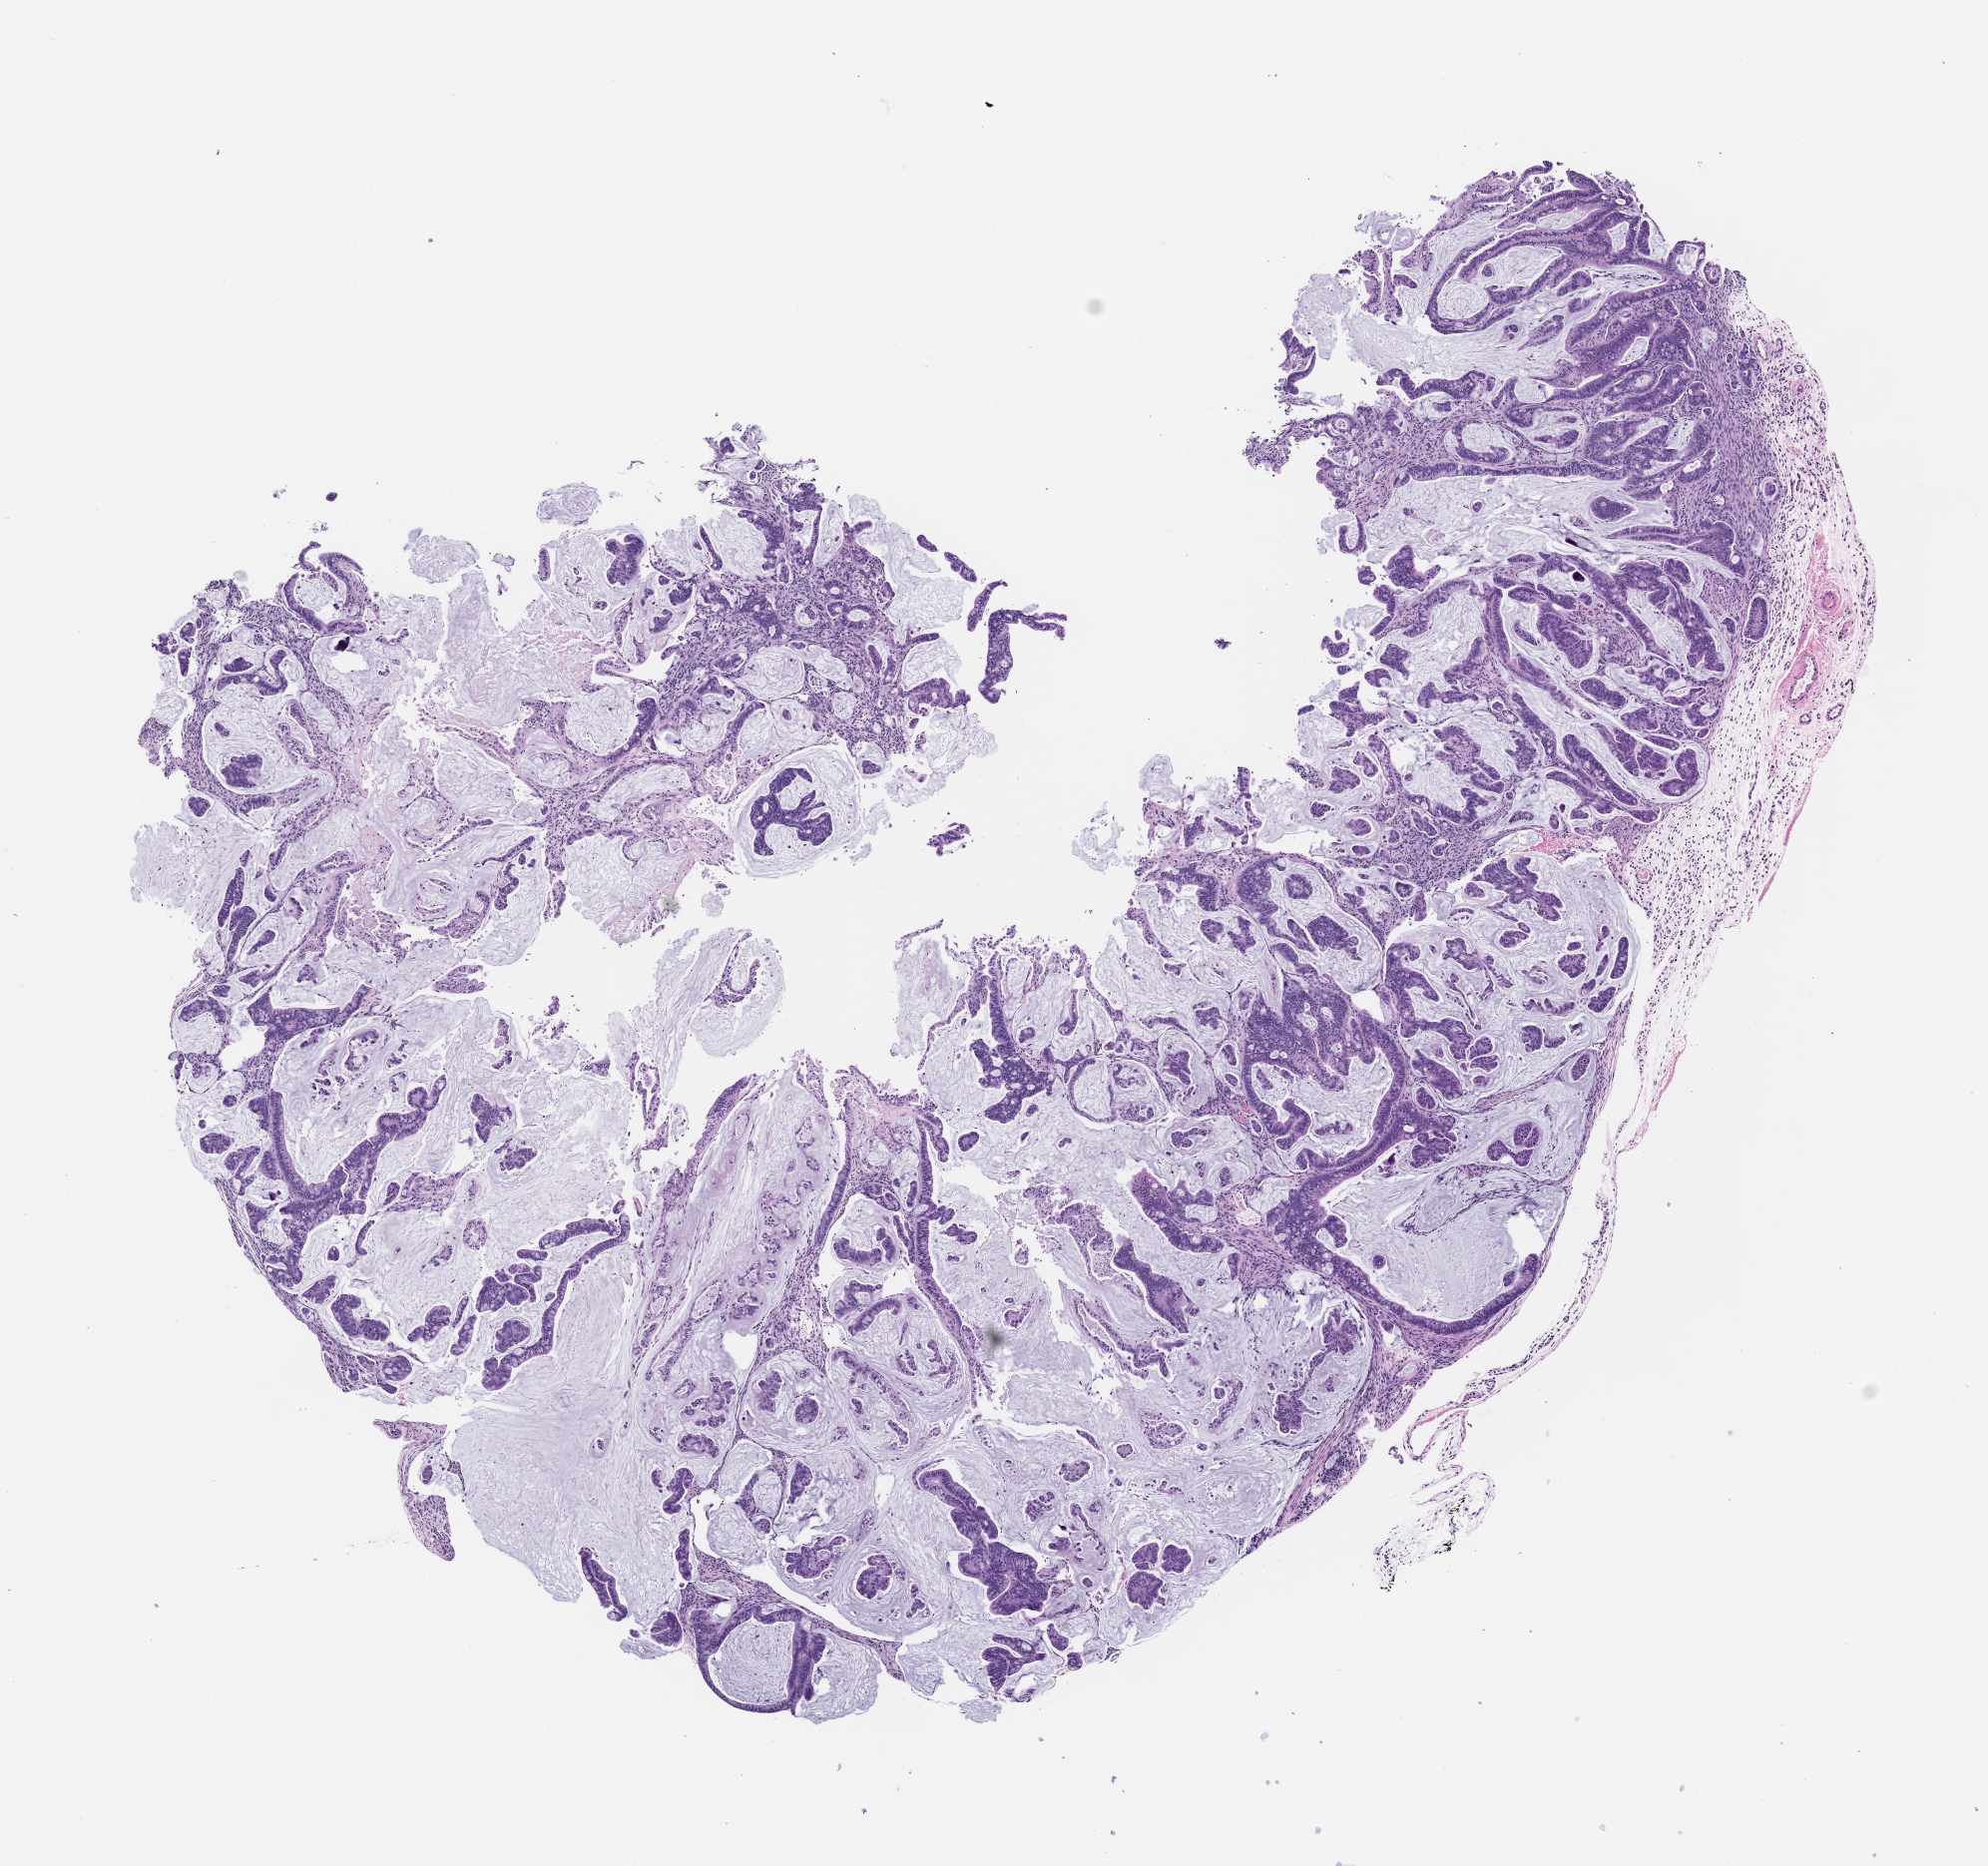
Haematoxylin and eosin whole-slide image of a patient-derived xenograft (PDX) tumor grown in a mouse, passage 2, a low-resolution overview of the entire scanned area, about 8.0 x 7.5 mm. Formalin-fixed paraffin-embedded section. Tumor site category: rectum.
Originating patient diagnosis: Rectal Adenocarcinoma.